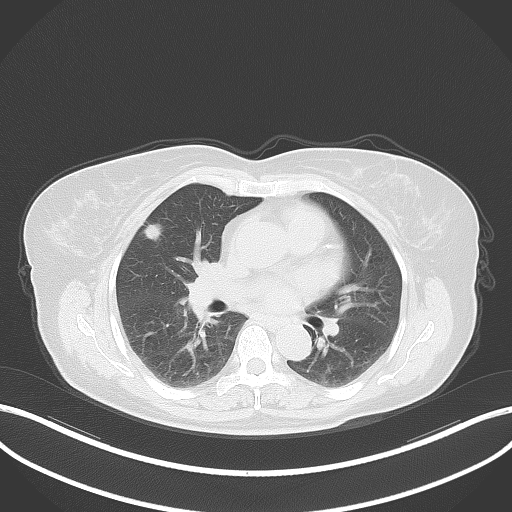
Chest CT, one axial slice; position 36 of 64 along the scan axis; lung window (W 1500 / L -600 HU); 3 mm slice thickness; 512 × 512 image matrix. Female patient, age 55 years. Case-level facts recorded for this patient, not image findings: clinical TNM (as recorded): T1b N0 M0.
Outlined on this slice (bounding box drawn by a radiologist):
- lung tumour (recorded histology: adenocarcinoma): bounding box [x1, y1, x2, y2] px = [140, 218, 166, 242]